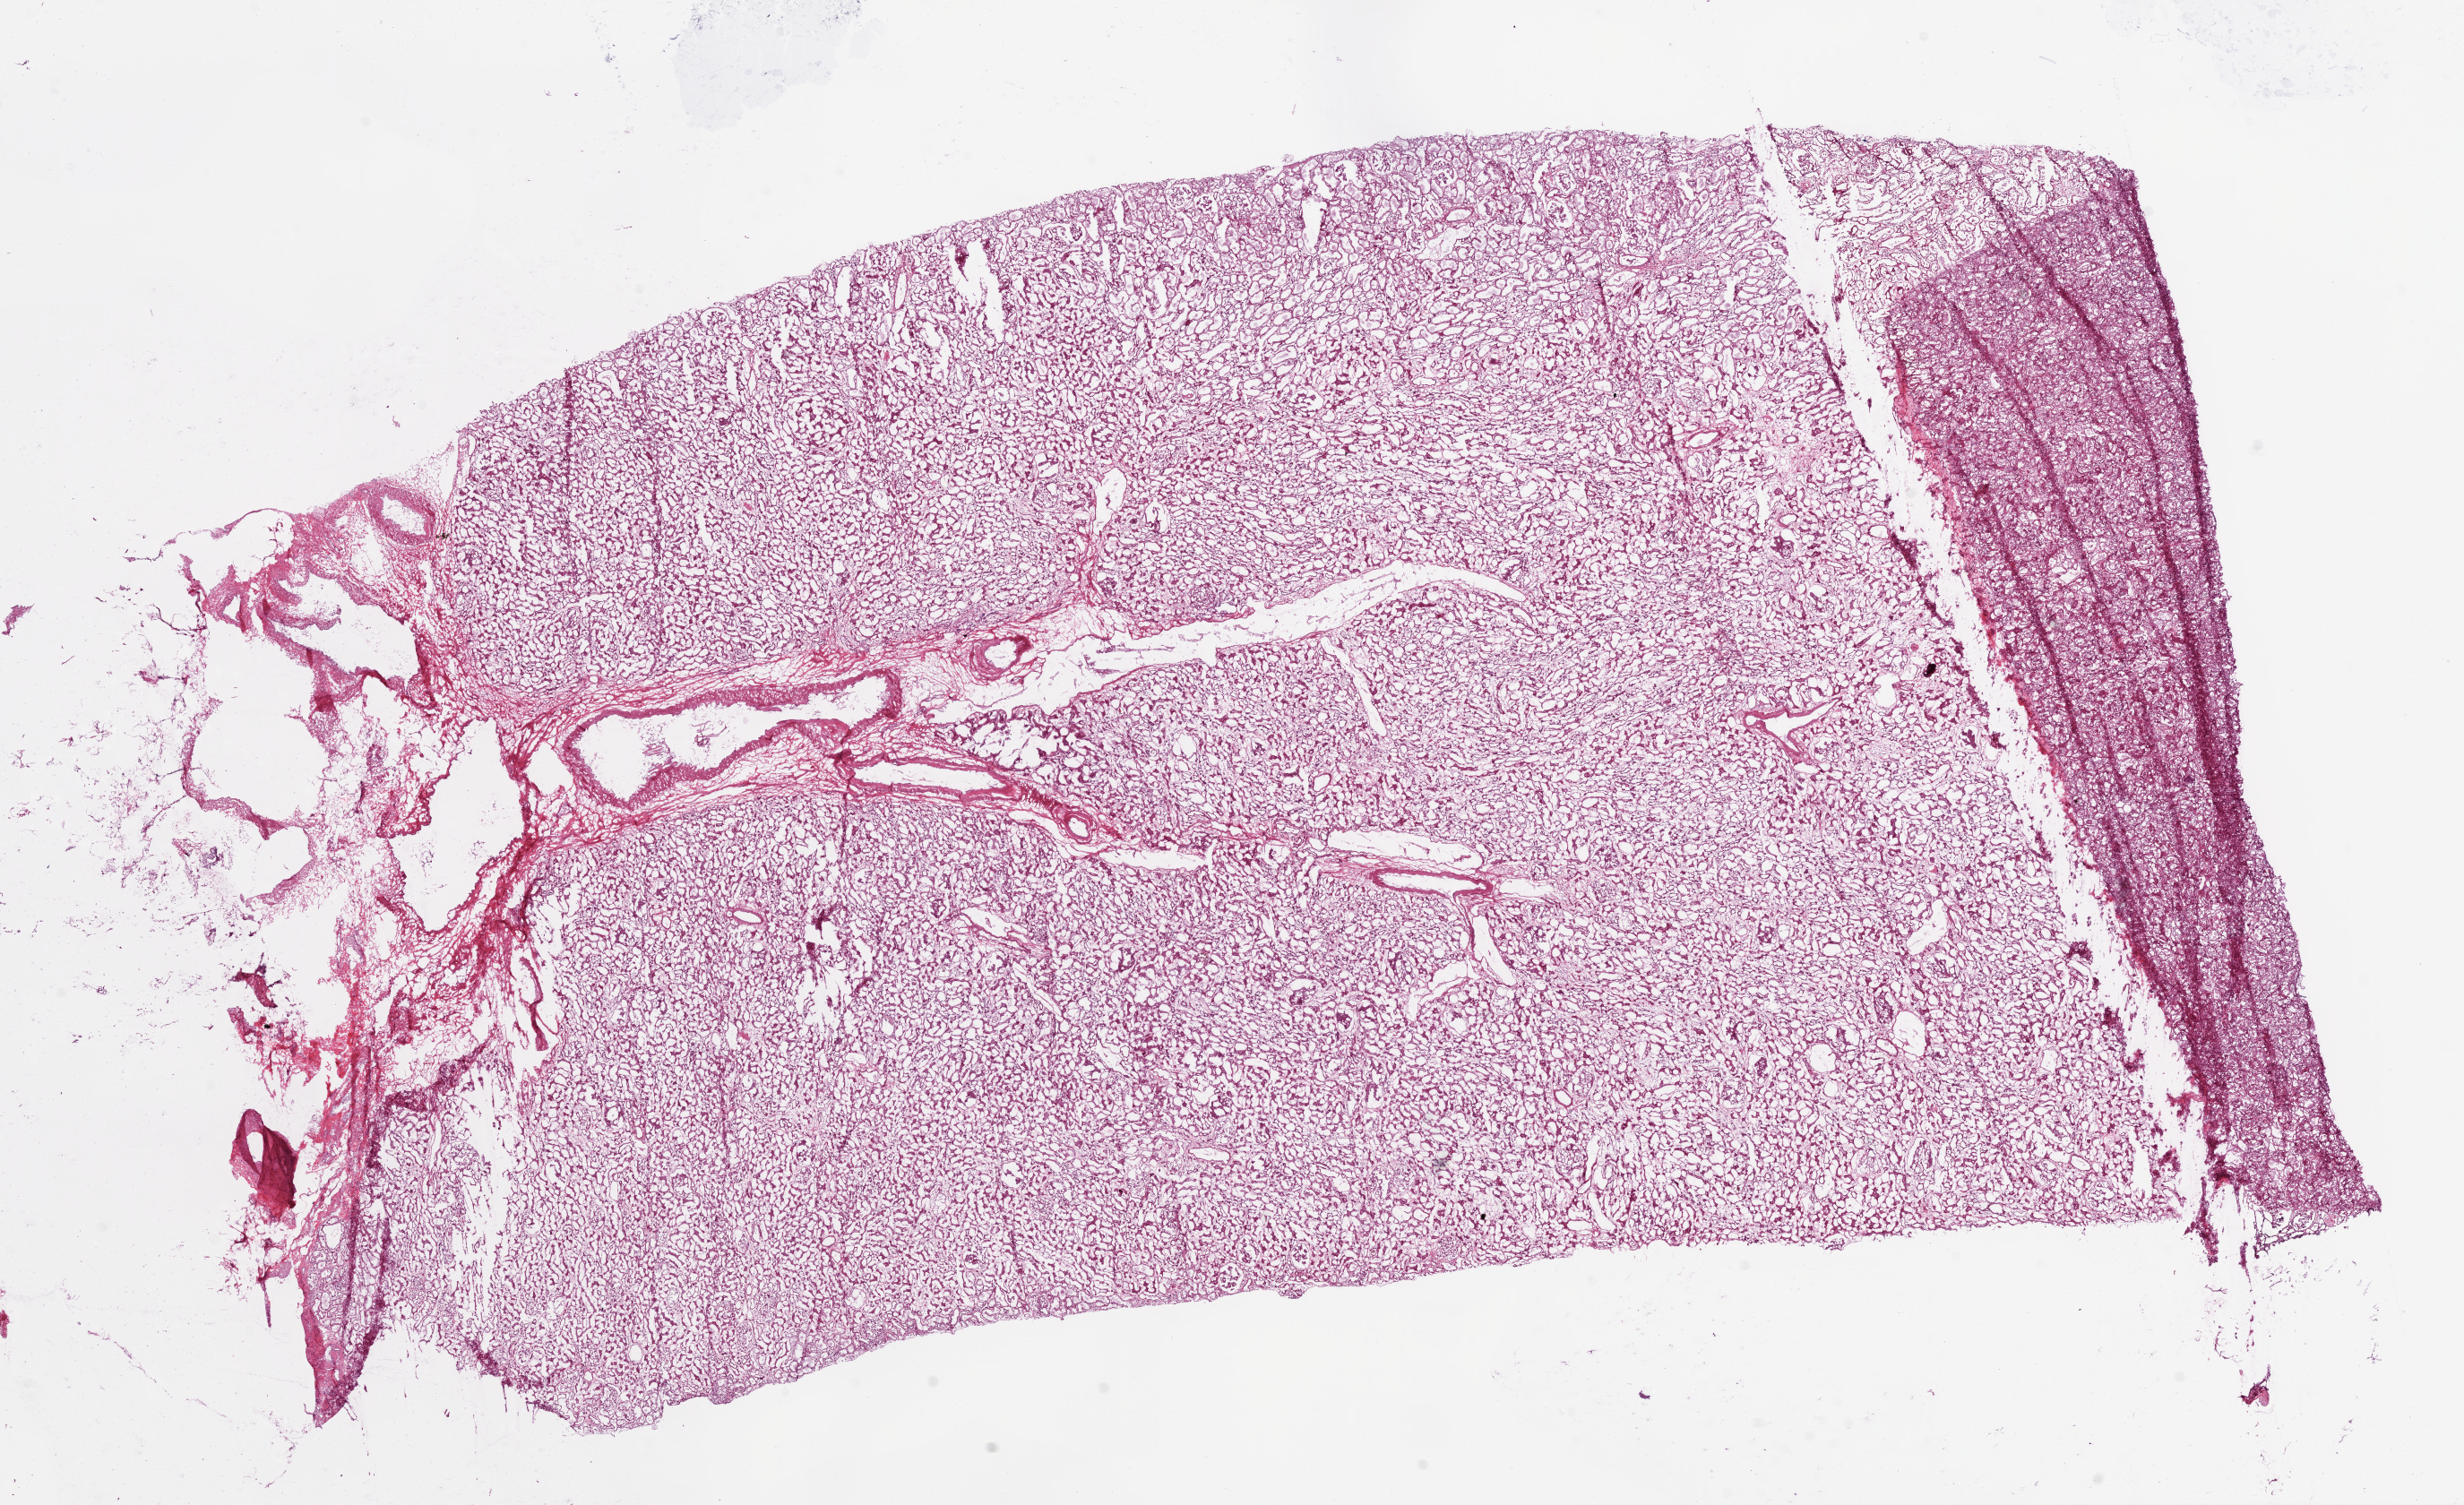
H&E whole-slide image, low-resolution overview of the scanned area, about 22.1 x 13.5 mm; frozen section from the bottom of the tissue portion; solid tissue normal (non-tumour tissue) sample from the kidney. Female patient; age at initial diagnosis 51 years.
* this section: solid tissue normal (non-tumour) sample from the same patient
* patient diagnosis: Clear cell adenocarcinoma, NOS